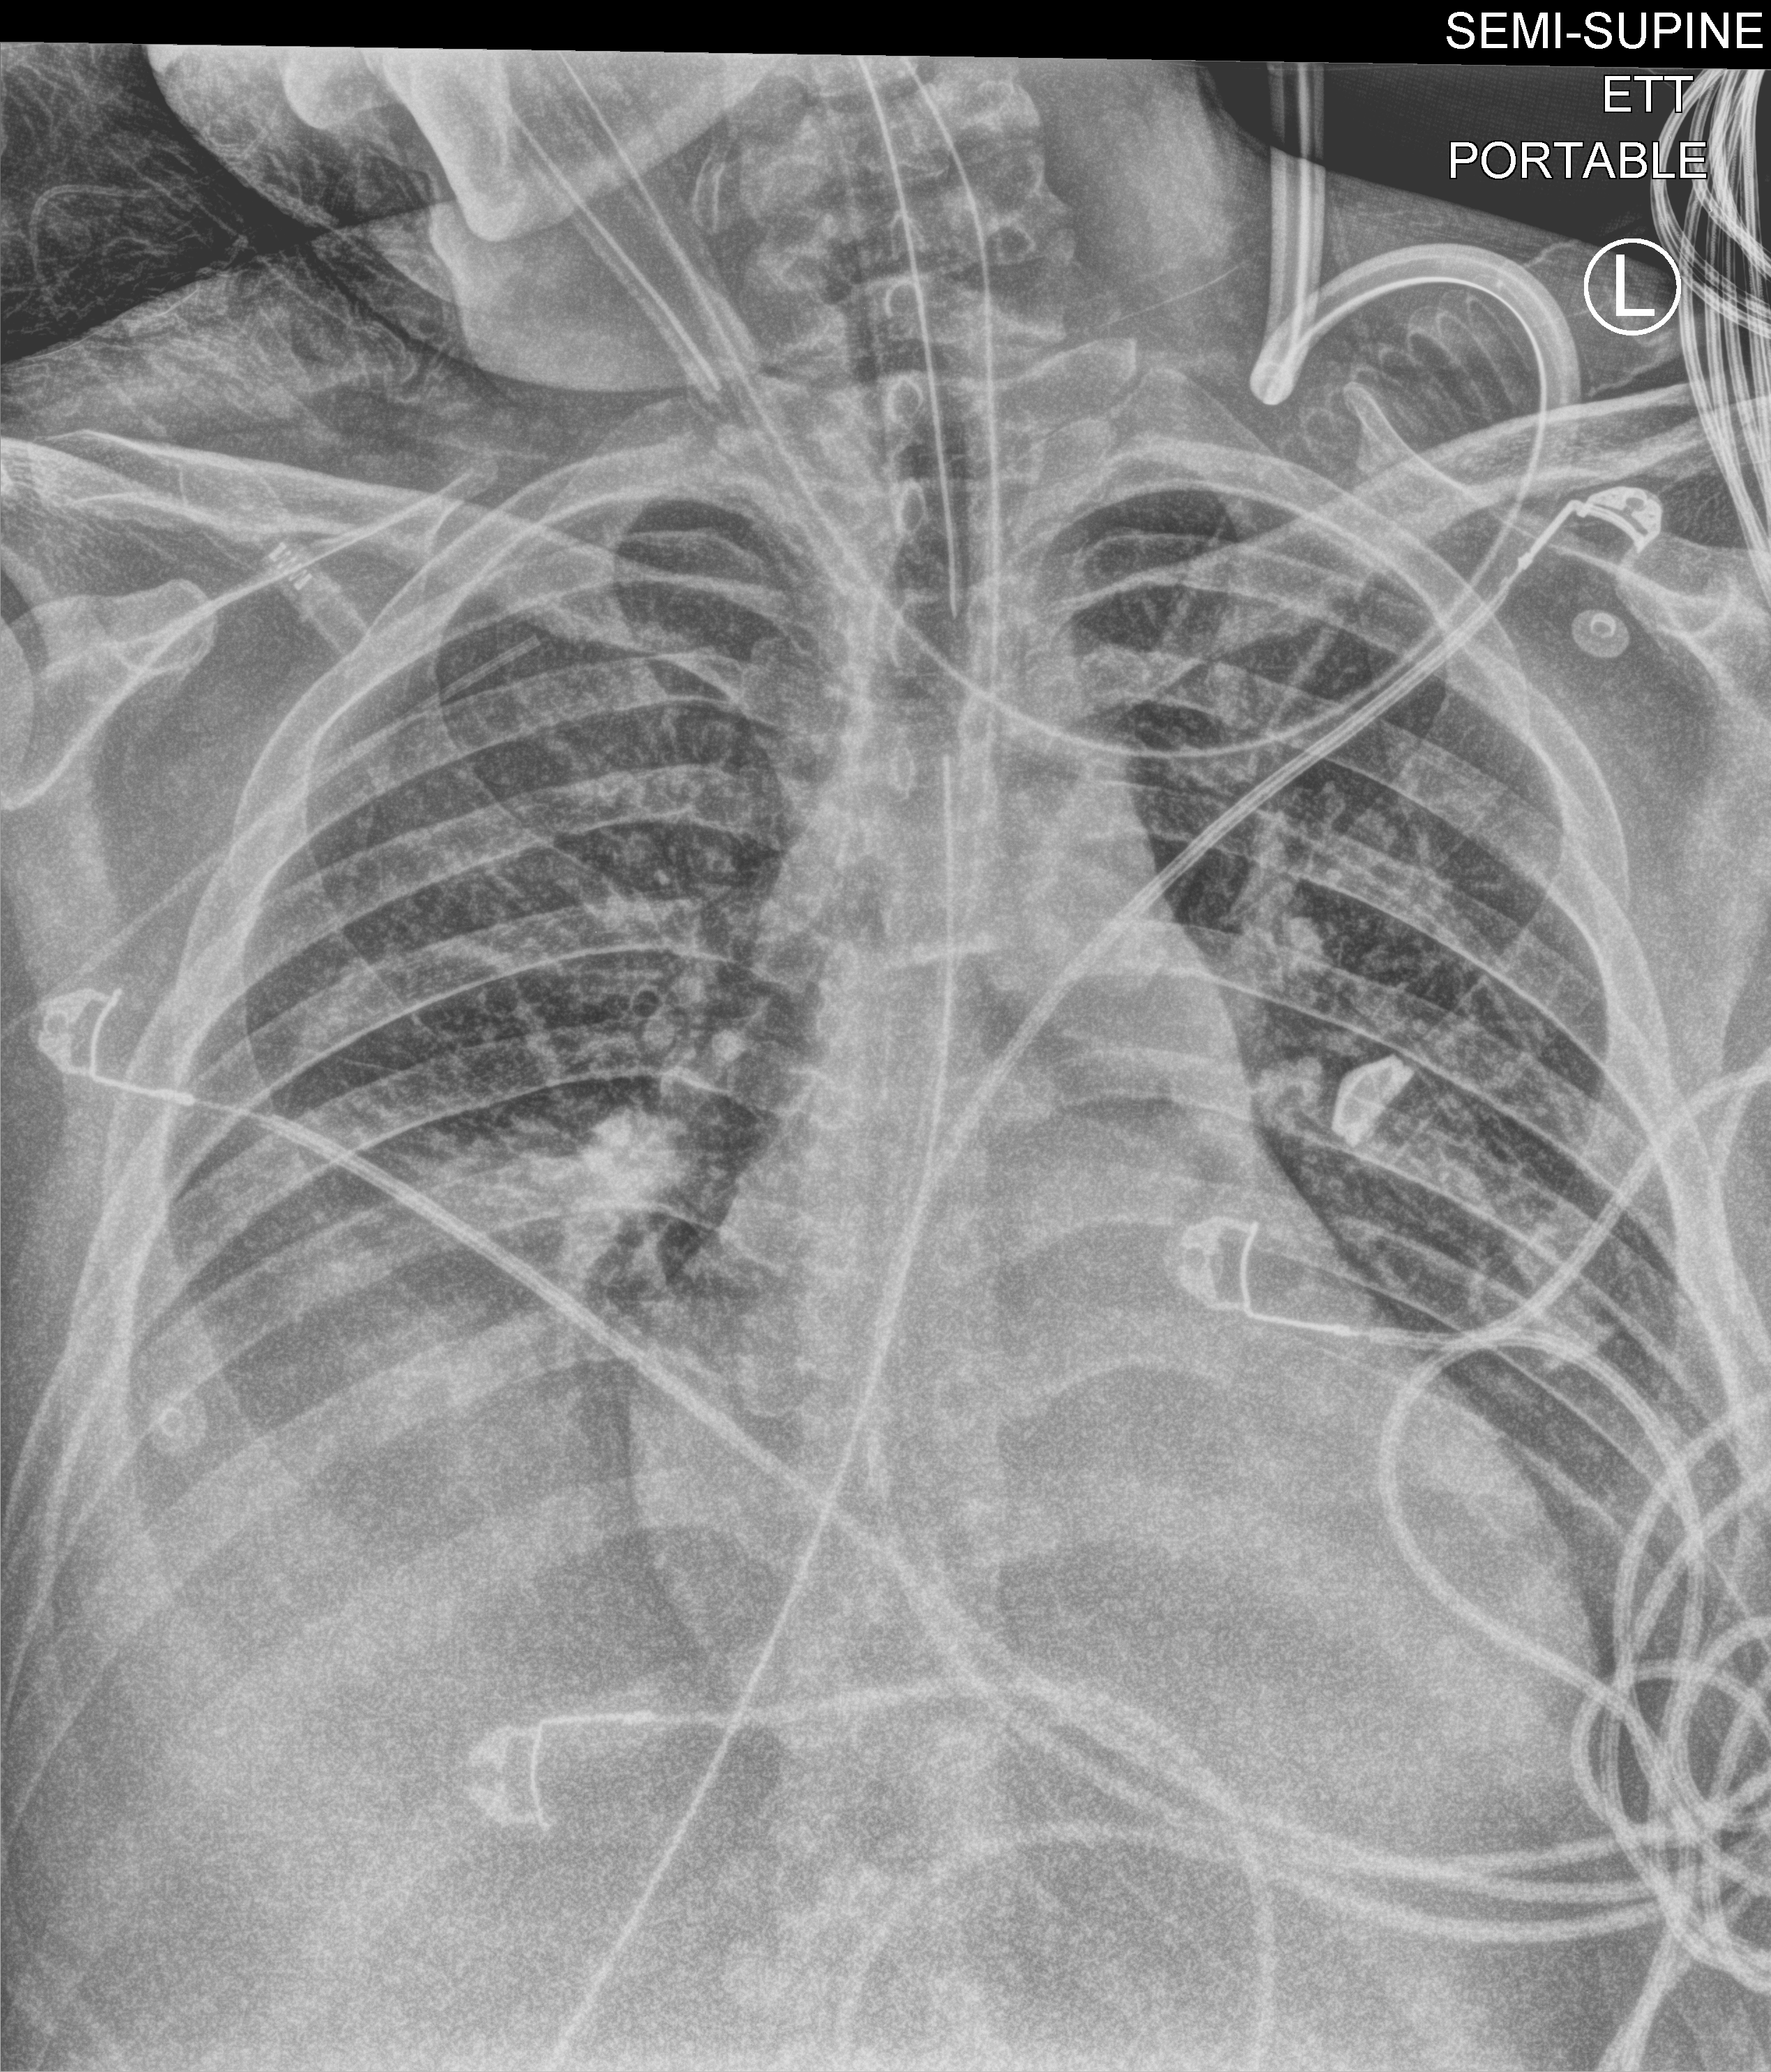
Chest X-ray (portable); anteroposterior (AP) projection. Patient hospitalised with COVID-19; male, aged 18–59 years.
Admission-level facts for this patient (not findings on this image; timing relative to this image not recorded):
- admitted to intensive care during this hospital stay: yes
- mechanically ventilated during this hospital stay: yes
- length of hospital stay: 61 days